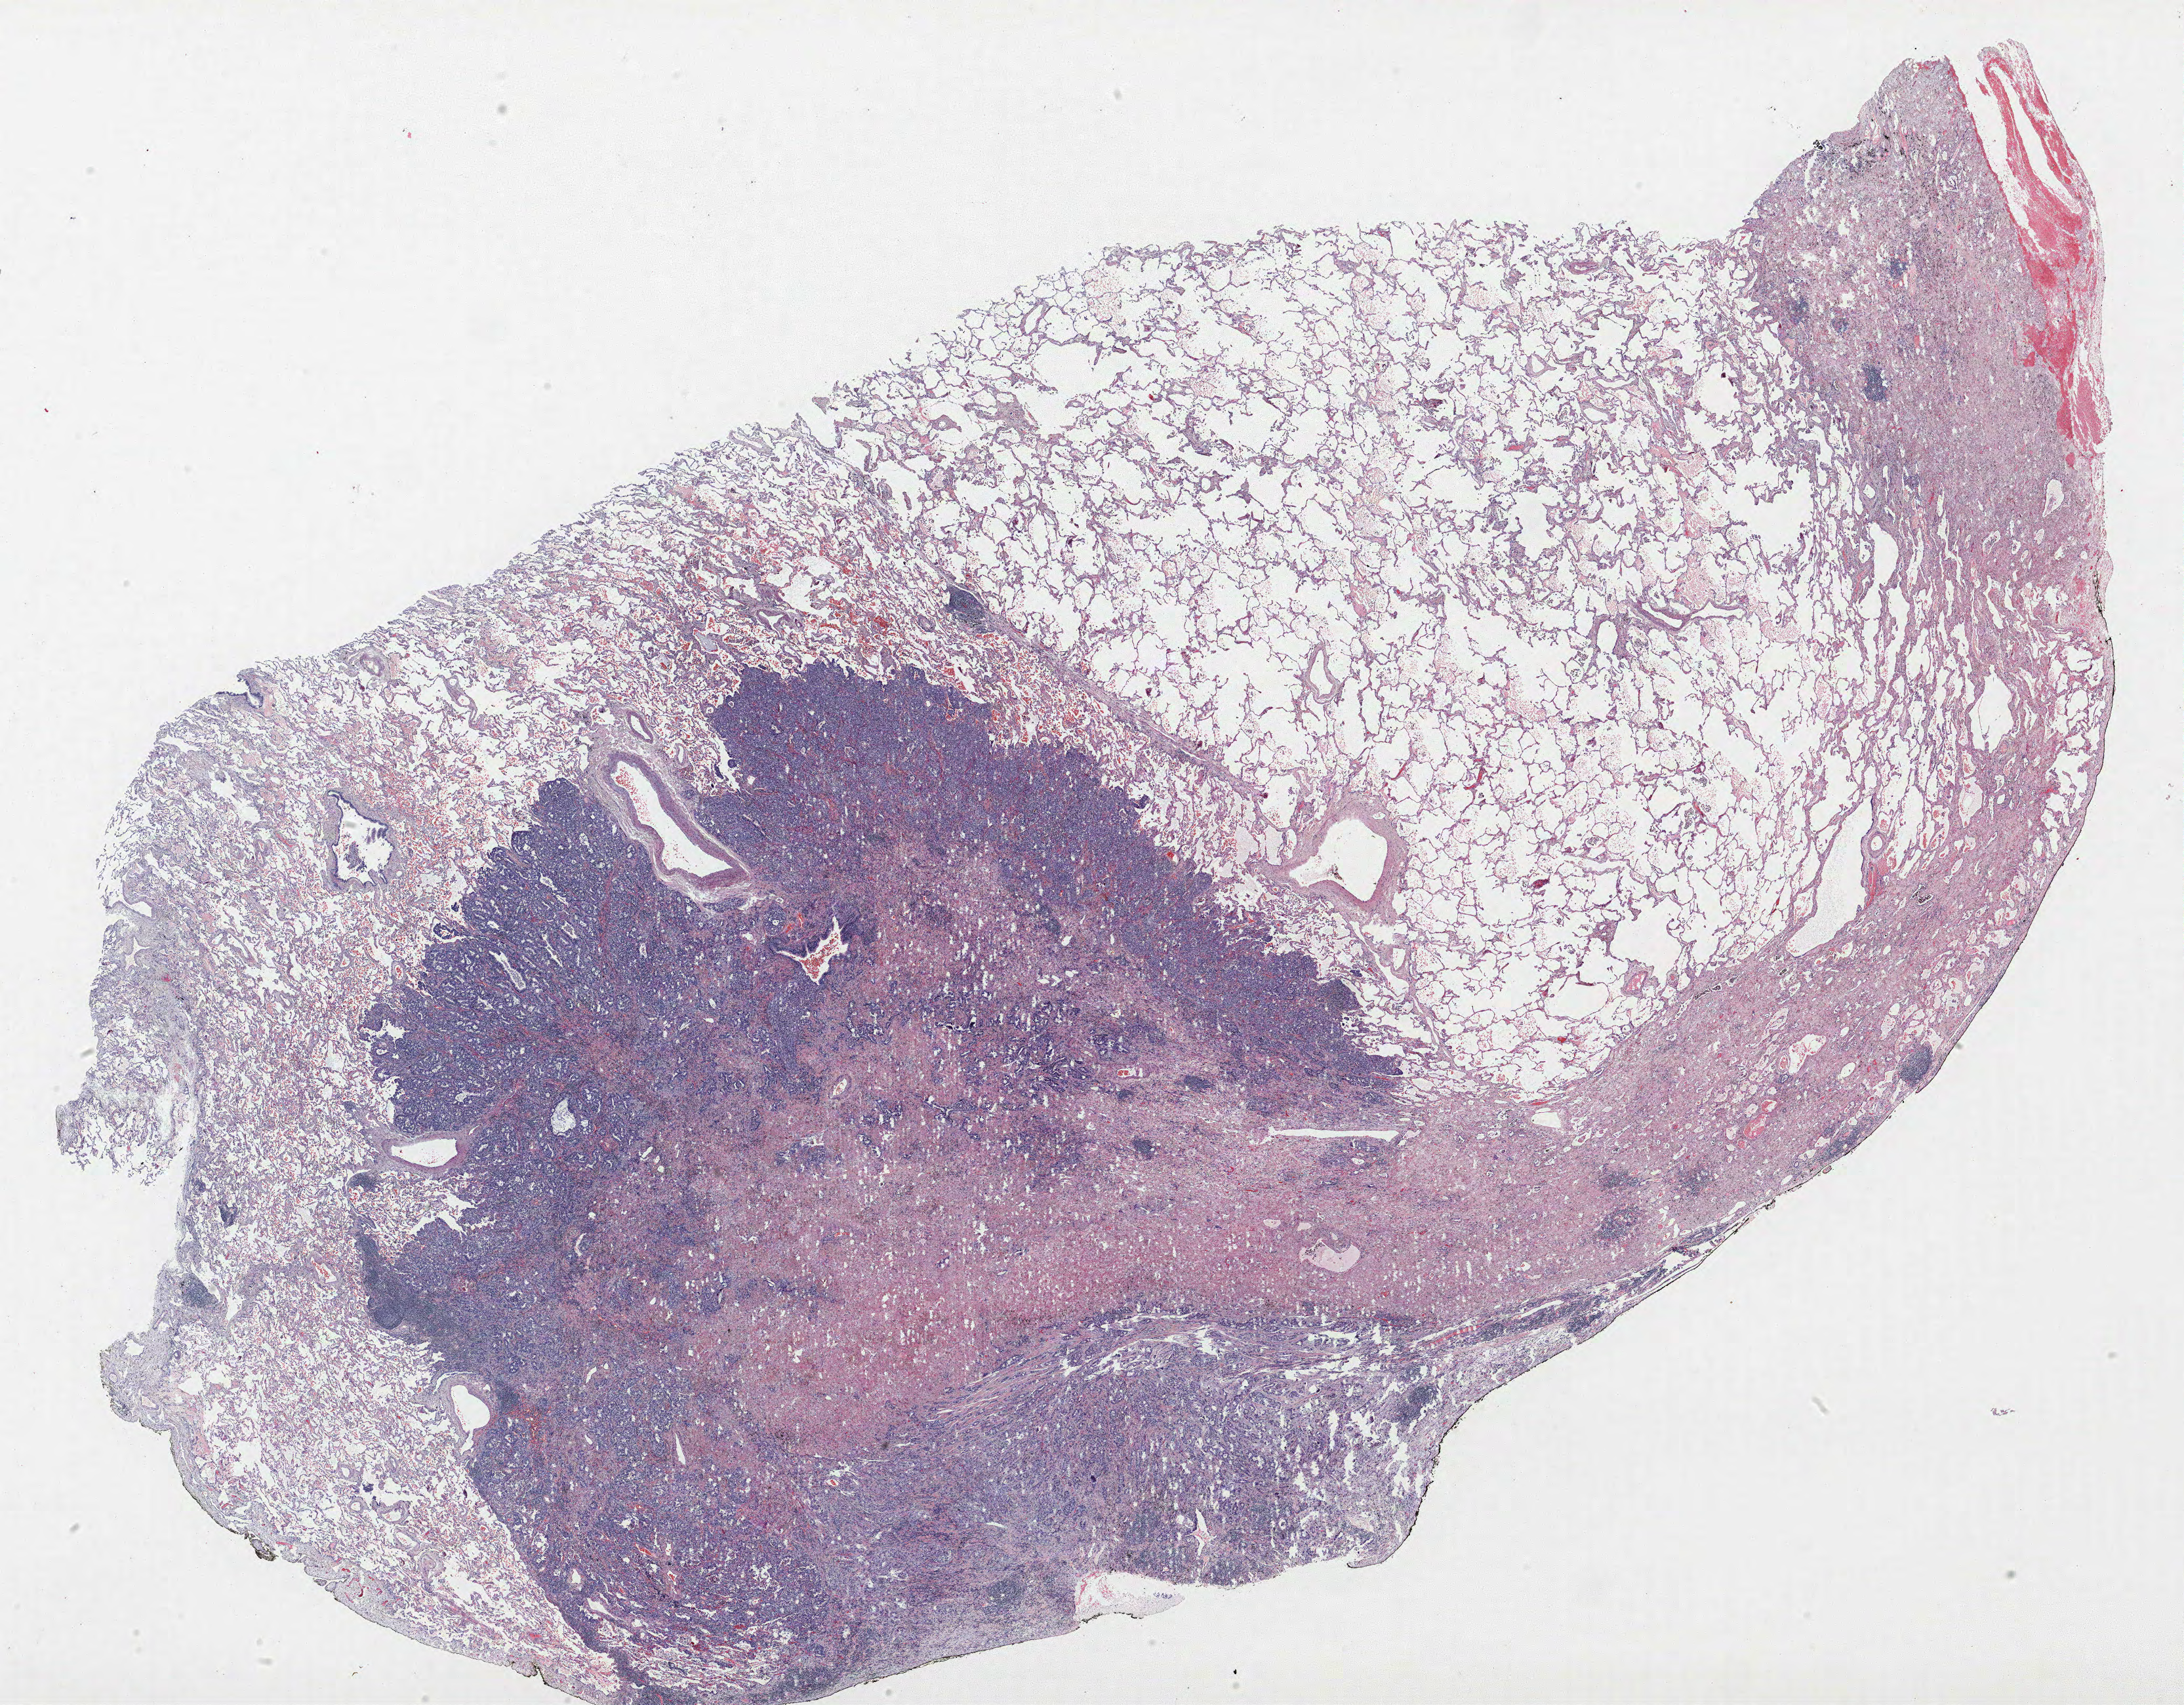
Whole-slide histology image, H&E — low-resolution overview of the scanned area, about 26.6 x 20.8 mm; formalin-fixed paraffin-embedded (FFPE) section; lung. Female patient, aged 67 at enrolment. Current smoker at enrolment. Grade: moderately differentiated (G2).
Participant's lung-cancer diagnosis: Adenocarcinoma, NOS. Stage (AJCC 6th edition): IA. Primary tumour location (clinical record): right upper lobe. Tumour size (pathology): 14 mm. Note: participant had 2 primary lung cancers recorded; fields above describe the first.